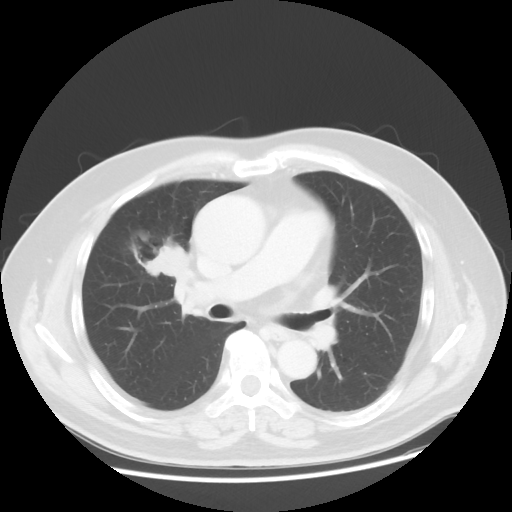
Chest CT, one axial slice. Position 25 of 48 along the scan axis. Reconstruction kernel STANDARD. Lung window (W 1500 / L -600 HU). 512 × 512 image matrix. Male patient, age 60 years. From the clinical record (not read from this slice): clinical TNM (as recorded): T2 N3 M0; histopathological grade: G2-3.
Outlined on this slice (rectangle marked by the reading radiologist):
- lung tumour (recorded histology: adenocarcinoma): box from (x=120, y=227) to (x=191, y=303) px